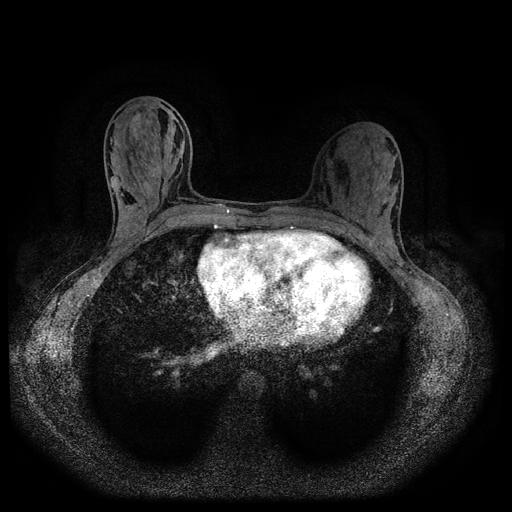
Breast MRI (dynamic contrast-enhanced, multi-phase), one axial slice. Position 47 of 116 along the scan axis. Dynamic contrast-enhanced series, time point 2 of 5 at this slice position (early post-contrast). 1.5 T. TE 2.7 ms, TR 5.4 ms. 512 × 512 image matrix. Female patient, age 32 years.
Structures marked on this image (semi-automatically segmented with operator editing):
- breast lesion (labelled benign in the annotation): bounding box [x1, y1, x2, y2] px = [124, 112, 145, 141]